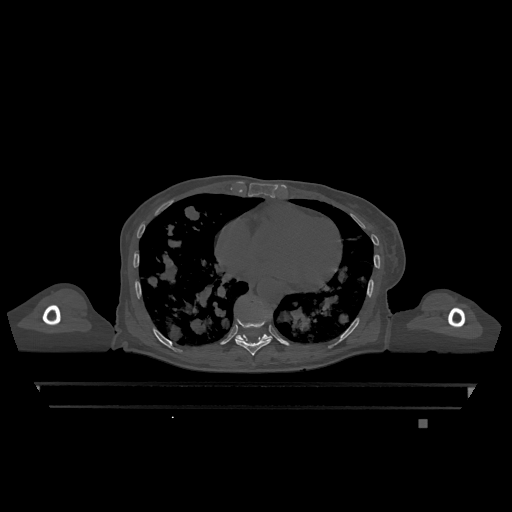
CT including the spine, one axial slice; slice 677 of 1317 in the series (ordered by position); bone window (W 1800 / L 400 HU); 512 × 512 image matrix, field of view 500 × 500 mm. Female patient, age 74 years. From the clinical record (not read from this slice): primary cancer: lung; vertebrae with lytic lesions (as recorded): T1, T4, T5, T6, L4, L5.
Annotated regions visible in this slice (semi-automatic segmentation, software-assisted and operator-edited):
- T10 vertebra: bounding box [x1, y1, x2, y2] px = [236, 334, 272, 340]
- T9 vertebra: [235, 307, 272, 356]